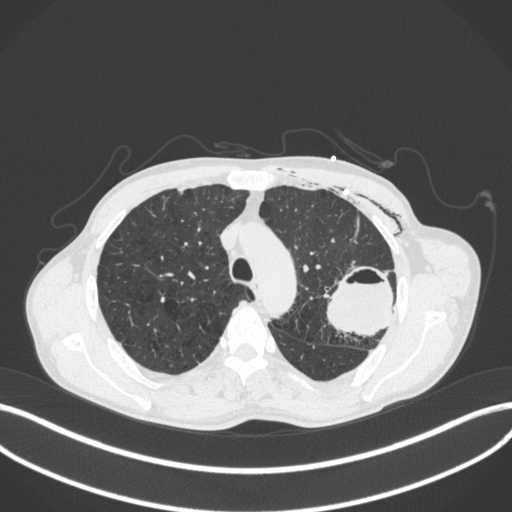
Chest CT, one axial slice. Position 298 of 416 along the scan axis. 120 kVp. Lung window (W 1500 / L -600 HU). 1 mm slice thickness. 512 × 512 image matrix, field of view 400 × 400 mm. Male patient, age 58 years. Case-level facts recorded for this patient, not image findings: clinical TNM (as recorded): T3 N0 M0.
Structures marked on this image (bounding box drawn by a radiologist):
- lung tumour (recorded histology: adenocarcinoma): bounding box <317,261,400,341> (left, top, right, bottom; pixels)